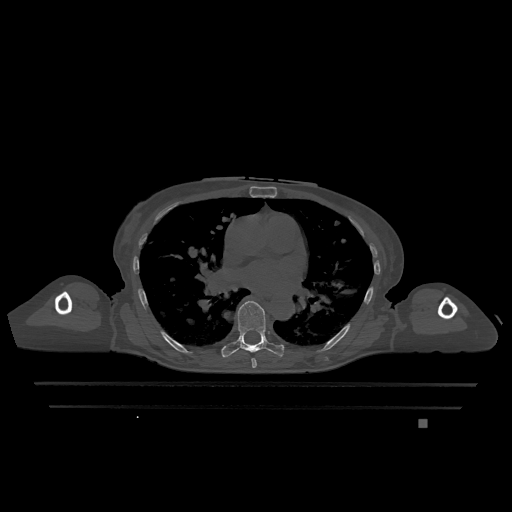
CT including the spine, one axial slice. Position 745 of 1317 along the scan axis. Bone window (W 1800 / L 400 HU). 512 × 512 image matrix, field of view 500 × 500 mm. Female patient, age 74 years. From the clinical record (not read from this slice): primary cancer: lung; vertebrae with lytic lesions (as recorded): T1, T4, T5, T6, L4, L5.
Annotated regions visible in this slice (semi-automatically segmented with operator editing):
- T6 vertebra: box from (x=252, y=358) to (x=257, y=368) px
- T7 vertebra: (x=221, y=301)–(x=284, y=358)